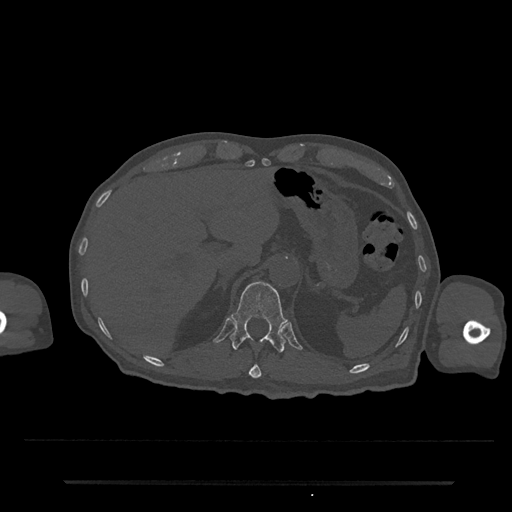
CT including the spine, one axial slice; position 209 of 797 along the scan axis; 120 kVp; bone window (W 1800 / L 400 HU); 0.5 mm slice thickness; 512 × 512 image matrix, field of view 427 × 427 mm. Male patient, age 74 years. Case-level facts recorded for this patient, not image findings: primary cancer: prostate.
Structures marked on this image (semi-automatically segmented with operator editing):
- T11 vertebra: bounding box <249,363,261,379> (left, top, right, bottom; pixels)
- T12 vertebra: <230,281,287,353>